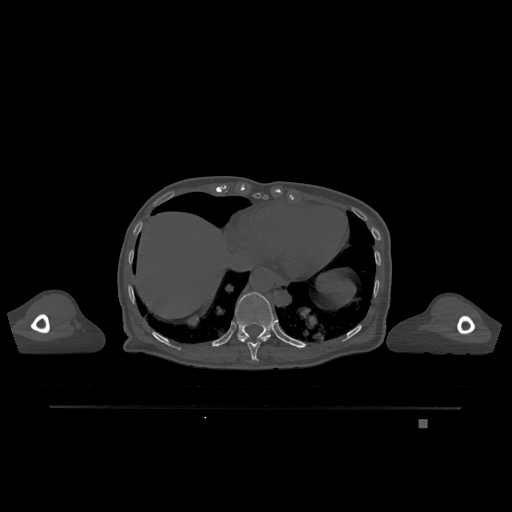
CT including the spine, one axial slice. Position 614 of 1317 along the scan axis. Bone window (W 1800 / L 400 HU). 512 × 512 image matrix. Female patient, age 74 years. From the clinical record (not read from this slice): primary cancer: lung.
Outlined on this slice (semi-automatic segmentation, software-assisted and operator-edited):
- T10 vertebra: bounding box (x1, y1, x2, y2) in pixels: (238, 337, 270, 361)
- T11 vertebra: (229, 292, 276, 340)